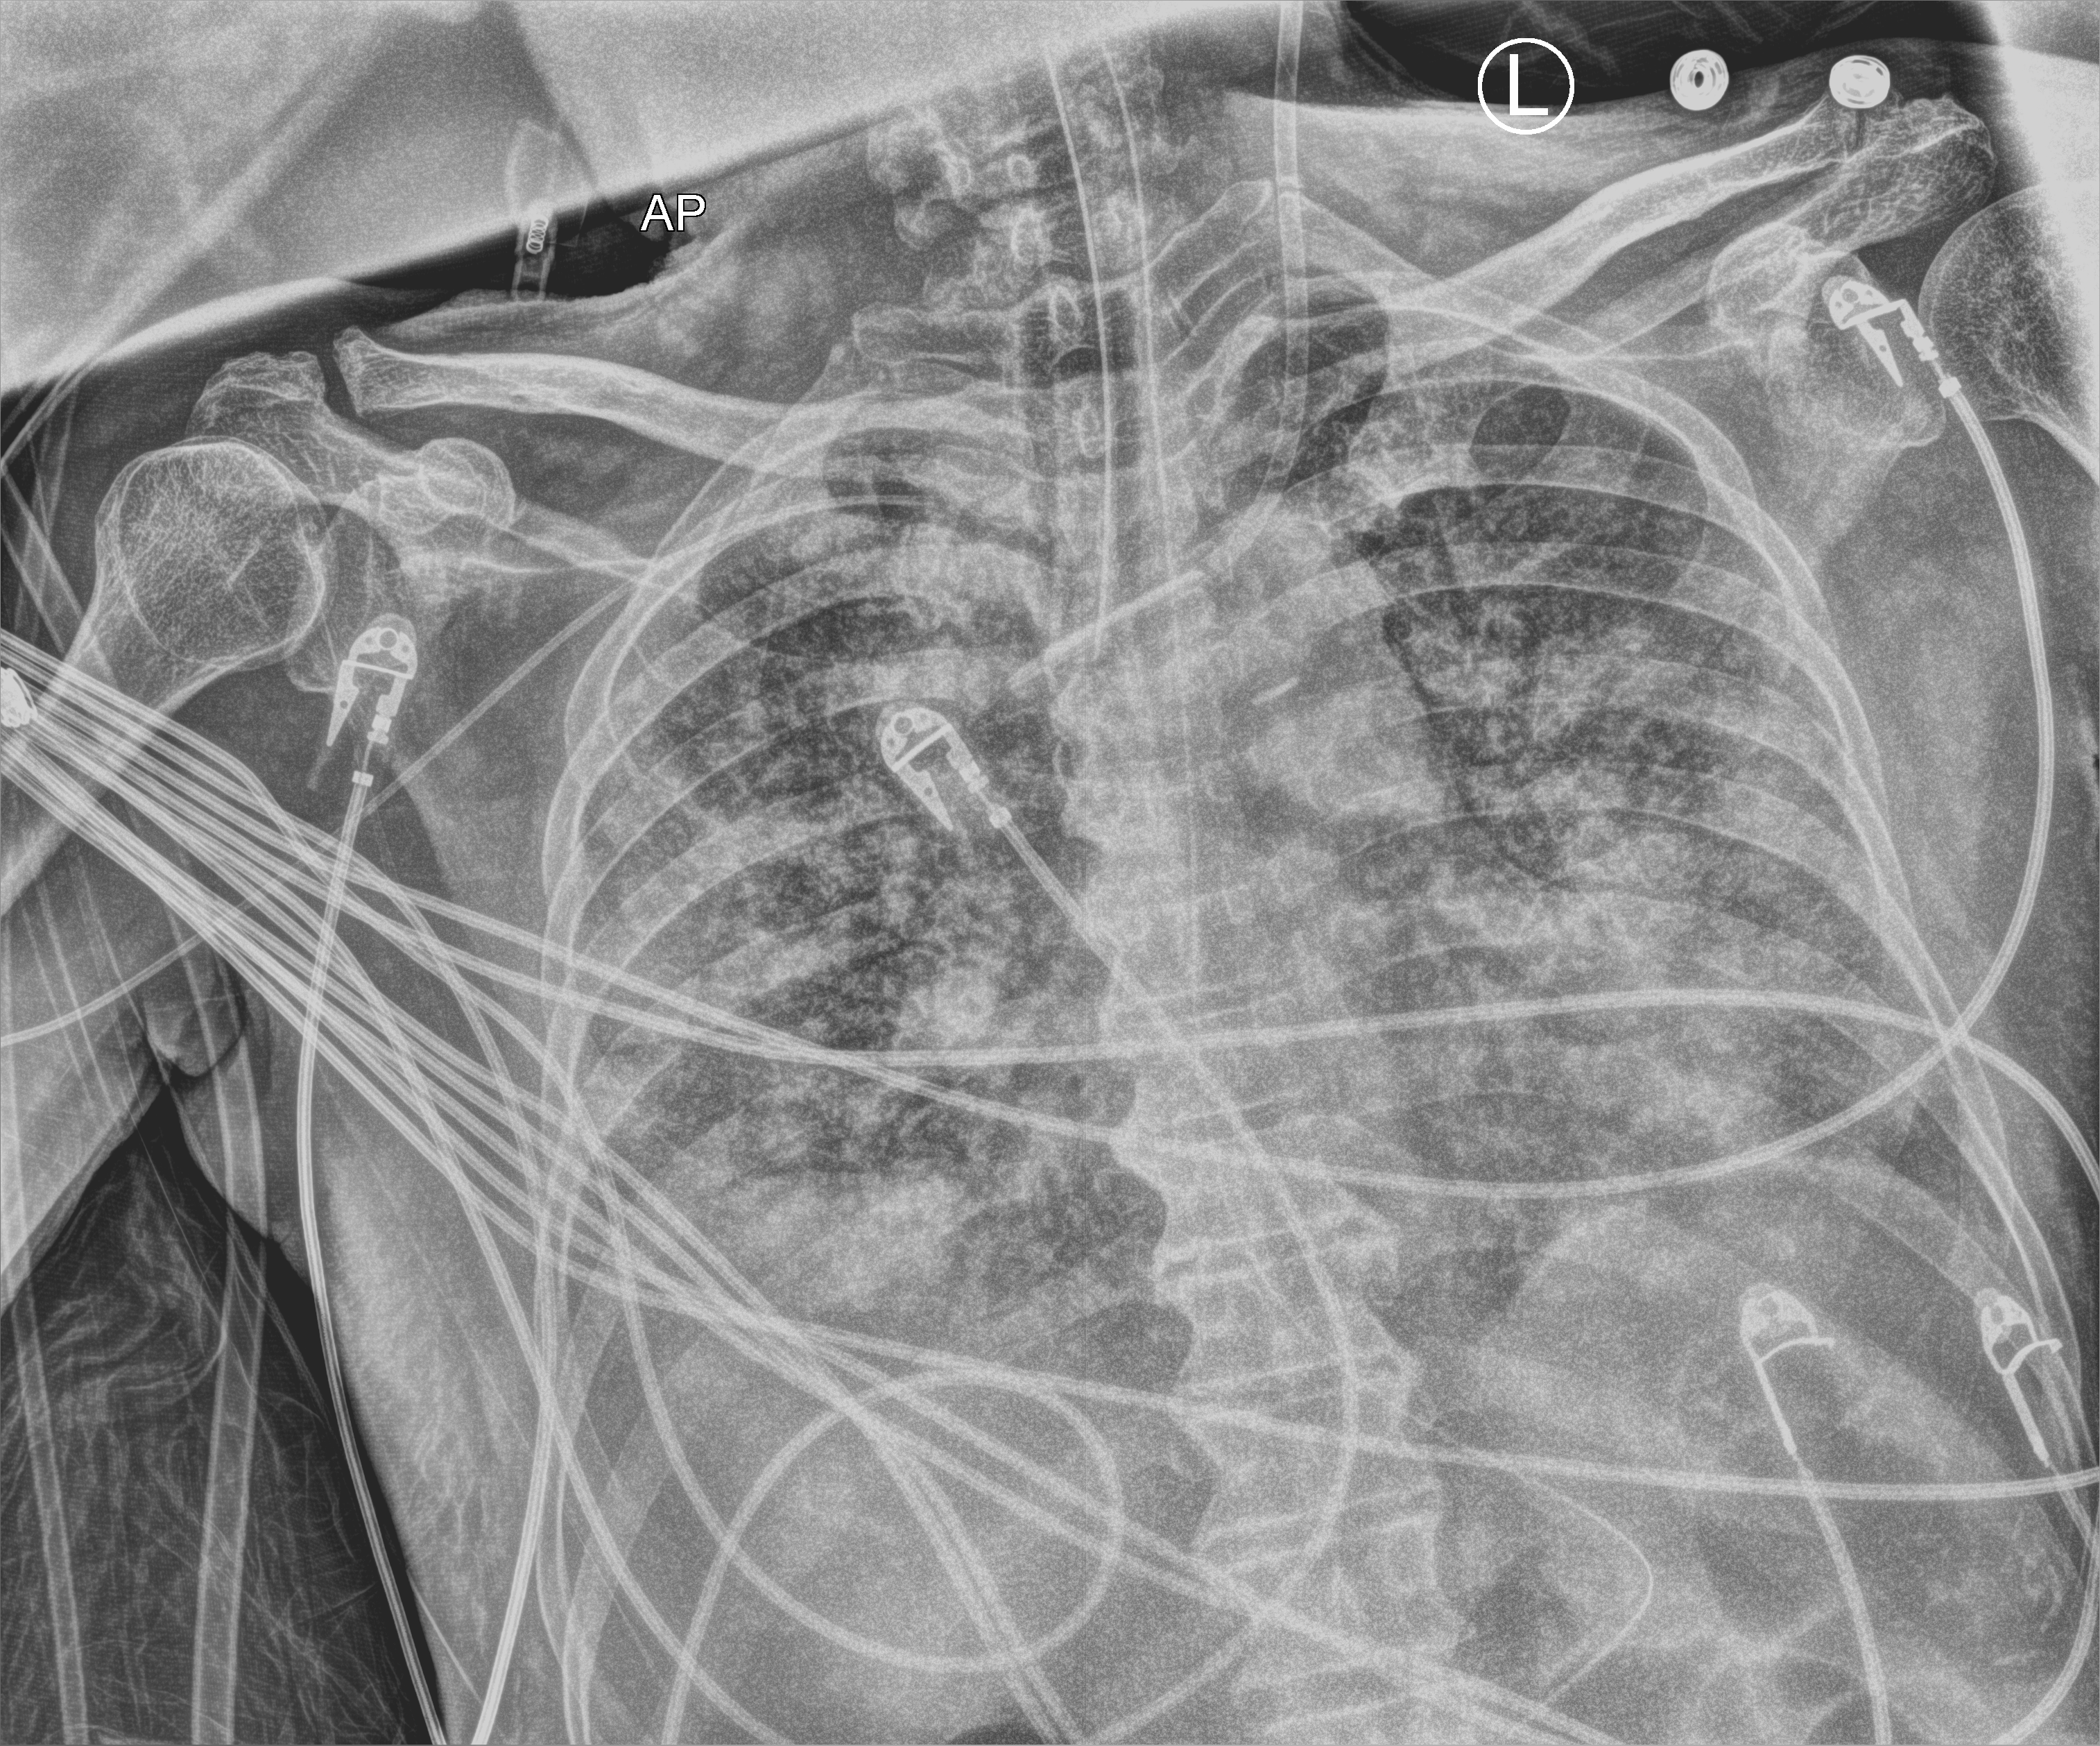
Chest X-ray (portable), anteroposterior (AP) projection. Male patient hospitalised with COVID-19, age 60–74 years.
Admission-level facts for this patient (not findings on this image; timing relative to this image not recorded): smoking status (admission record): never; COPD (admission record): no; diabetes (admission record): no.